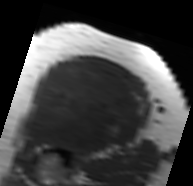
MRI of an extremity soft-tissue mass, one axial slice; position 51 of 91 along the scan axis; MR volume resampled by the dataset authors to the PET/CT grid (not the native acquisition matrix); 3.27 mm slice thickness; 193 × 186 image matrix, field of view 188 × 182 mm. Female patient. Case-level facts recorded for this patient, not image findings: histological type: malignant solitary fibrous tumor; grade: intermediate; site of the primary tumour: right thigh.
Annotated regions visible in this slice (expert contour drawn on MRI and transferred to this co-registered scan by the dataset authors):
- gross tumour volume including surrounding oedema: box from (x=21, y=60) to (x=146, y=152) px
- gross tumour volume (mass): (x=24, y=60)–(x=143, y=150)